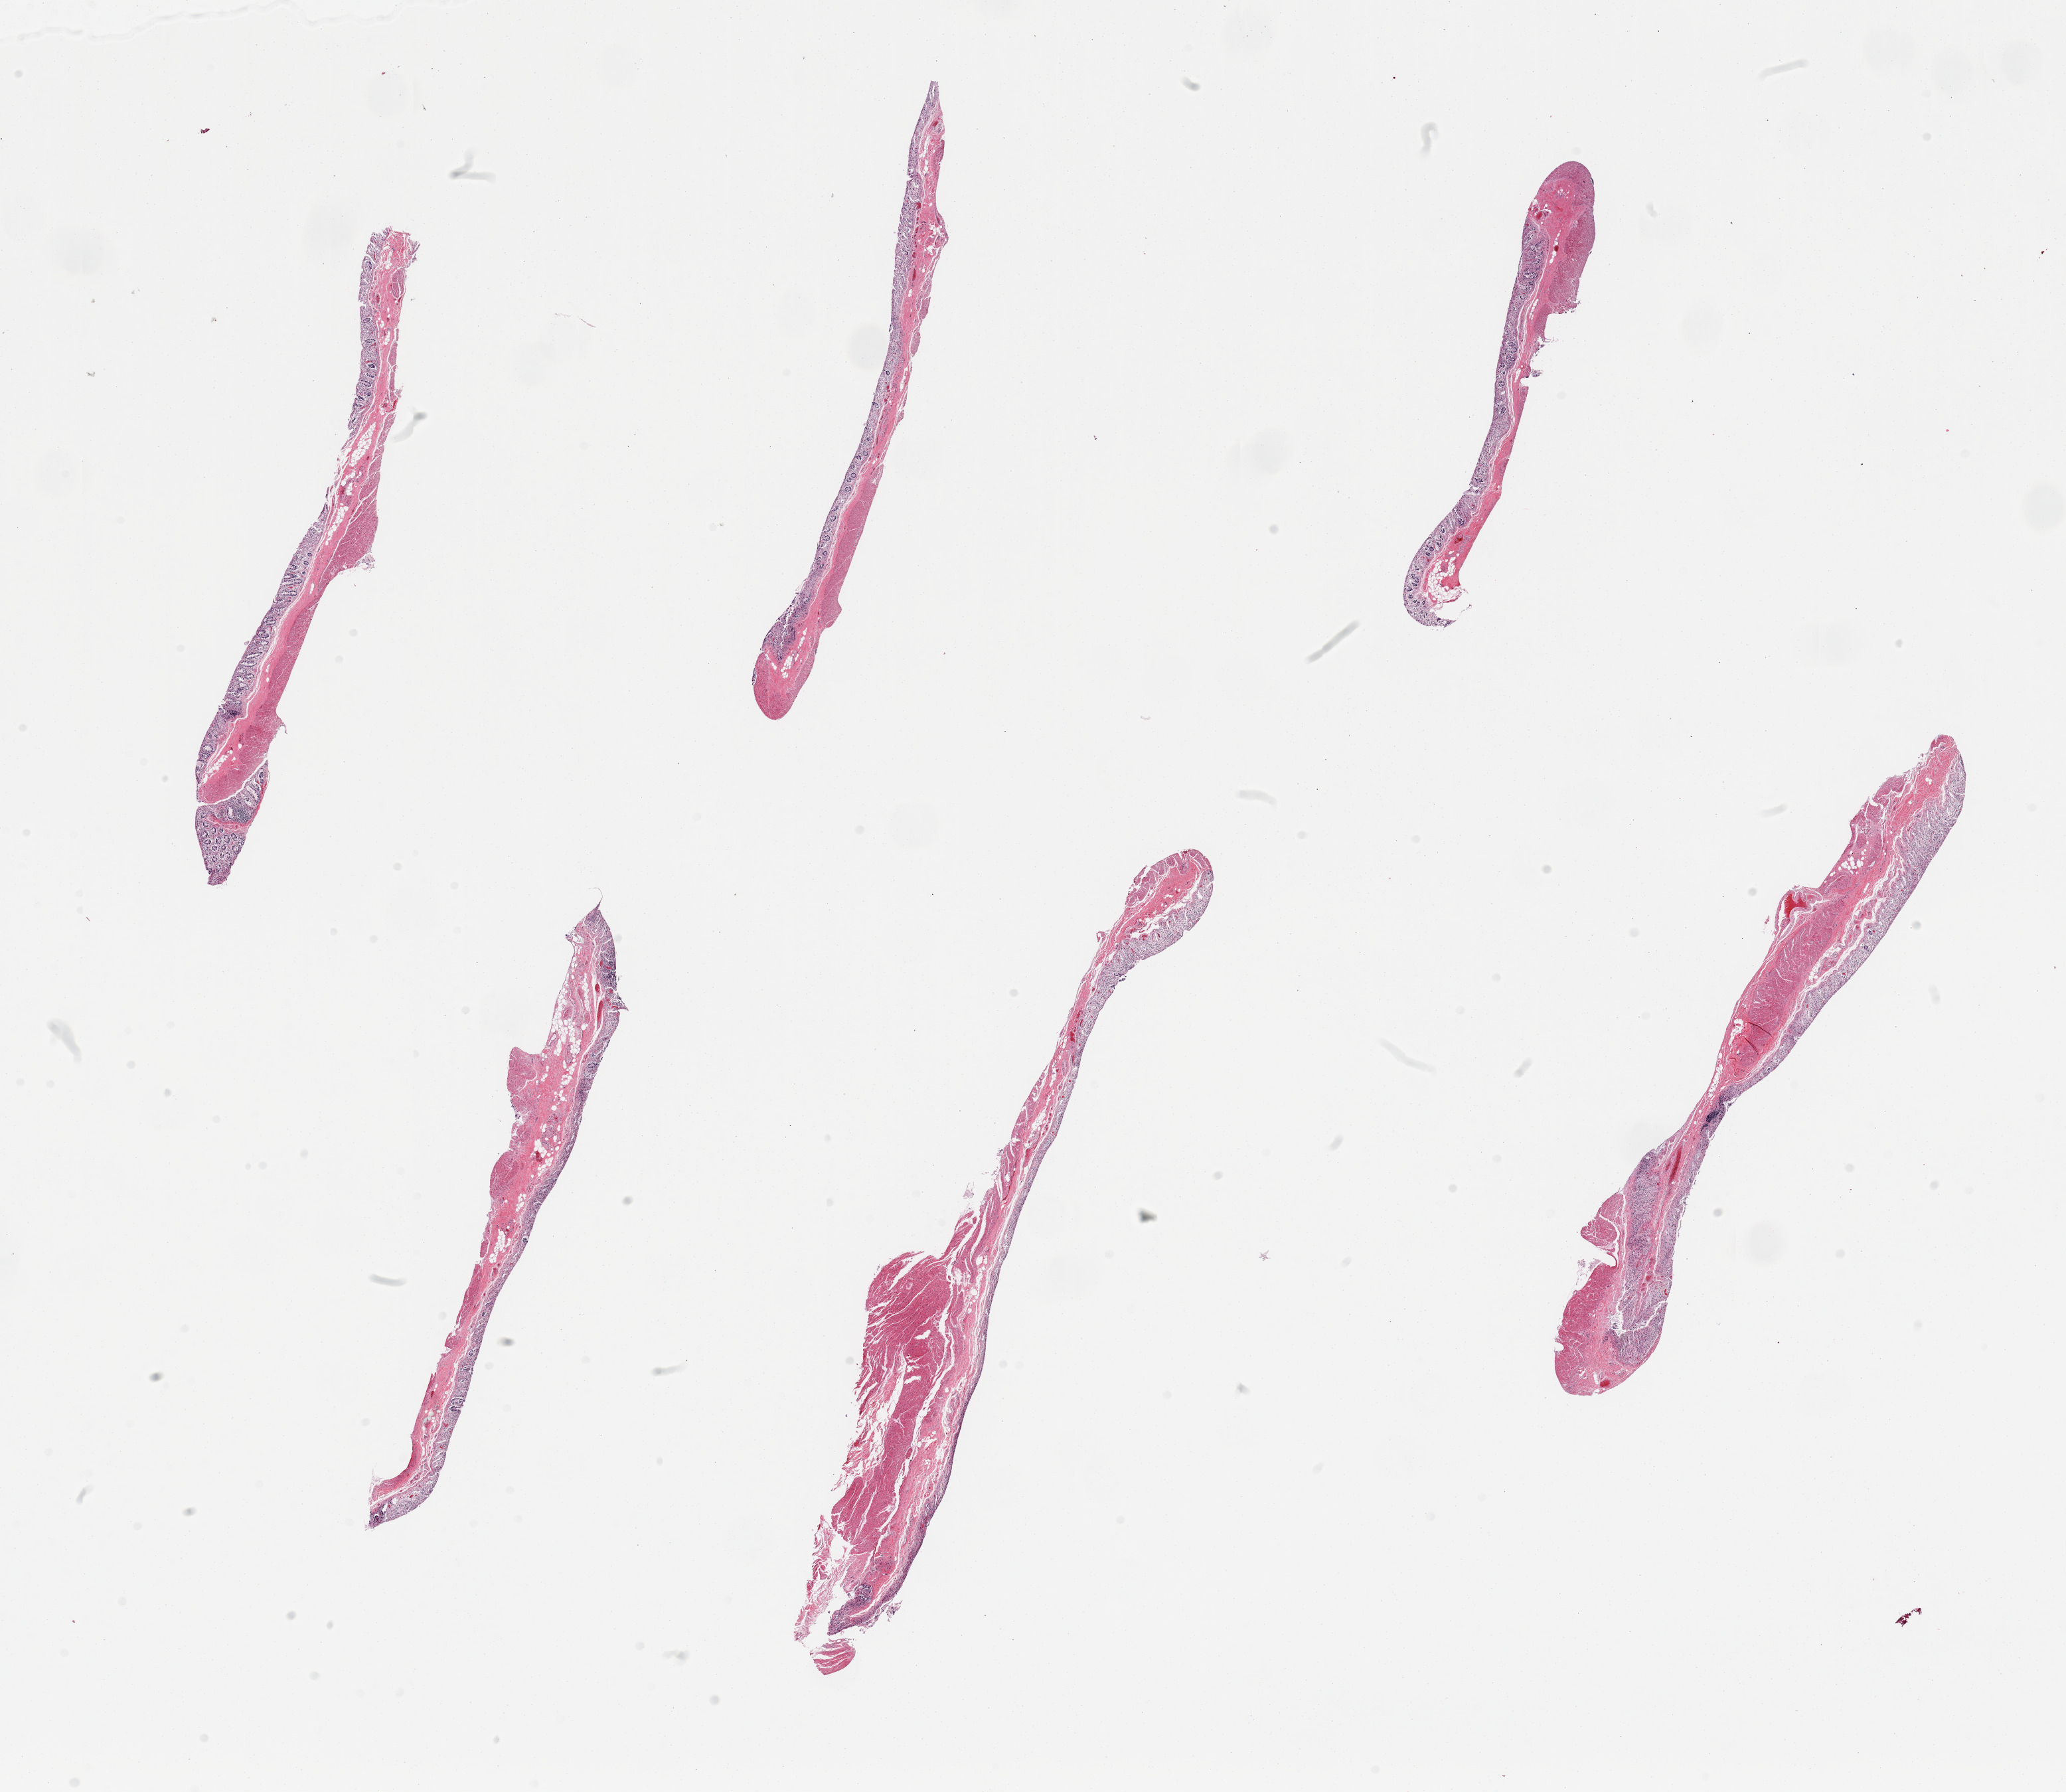
Haematoxylin and eosin whole-slide image — whole scanned area (about 24.6 x 21.3 mm) shown as a low-resolution overview. PAXgene-fixed paraffin-embedded (PFPE) section. Sampled site (target tissue): transverse colon. Tissue donor sample. Donor sex: male.
Reviewer comment on this tissue sample: 6 pieces mucosa up to ~0.4-0.5 mm, ~50% thickness; glandular elements of mucosa completely autolyzed.